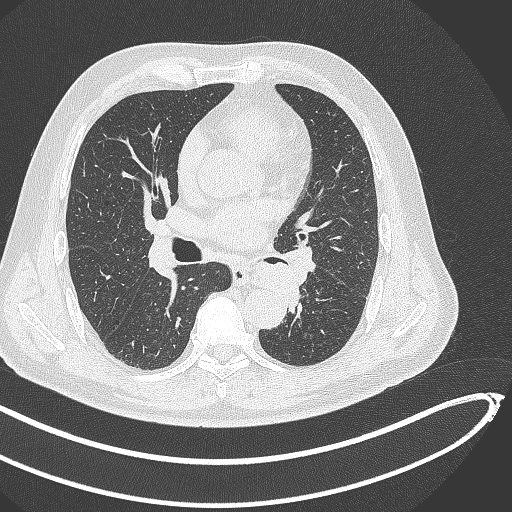
Chest CT, one axial slice; slice 252 of 468 in the series (ordered by position); reconstruction kernel B70f; lung window (W 1500 / L -600 HU); 1 mm slice thickness; 512 × 512 image matrix. Patient: male, 64 years. From the clinical record (not read from this slice): clinical TNM (as recorded): T1c N0 M0; histopathological grade: G2.
Annotated regions visible in this slice (bounding box drawn by a radiologist):
- lung tumour (recorded histology: squamous cell carcinoma): box from (x=246, y=260) to (x=300, y=311) px